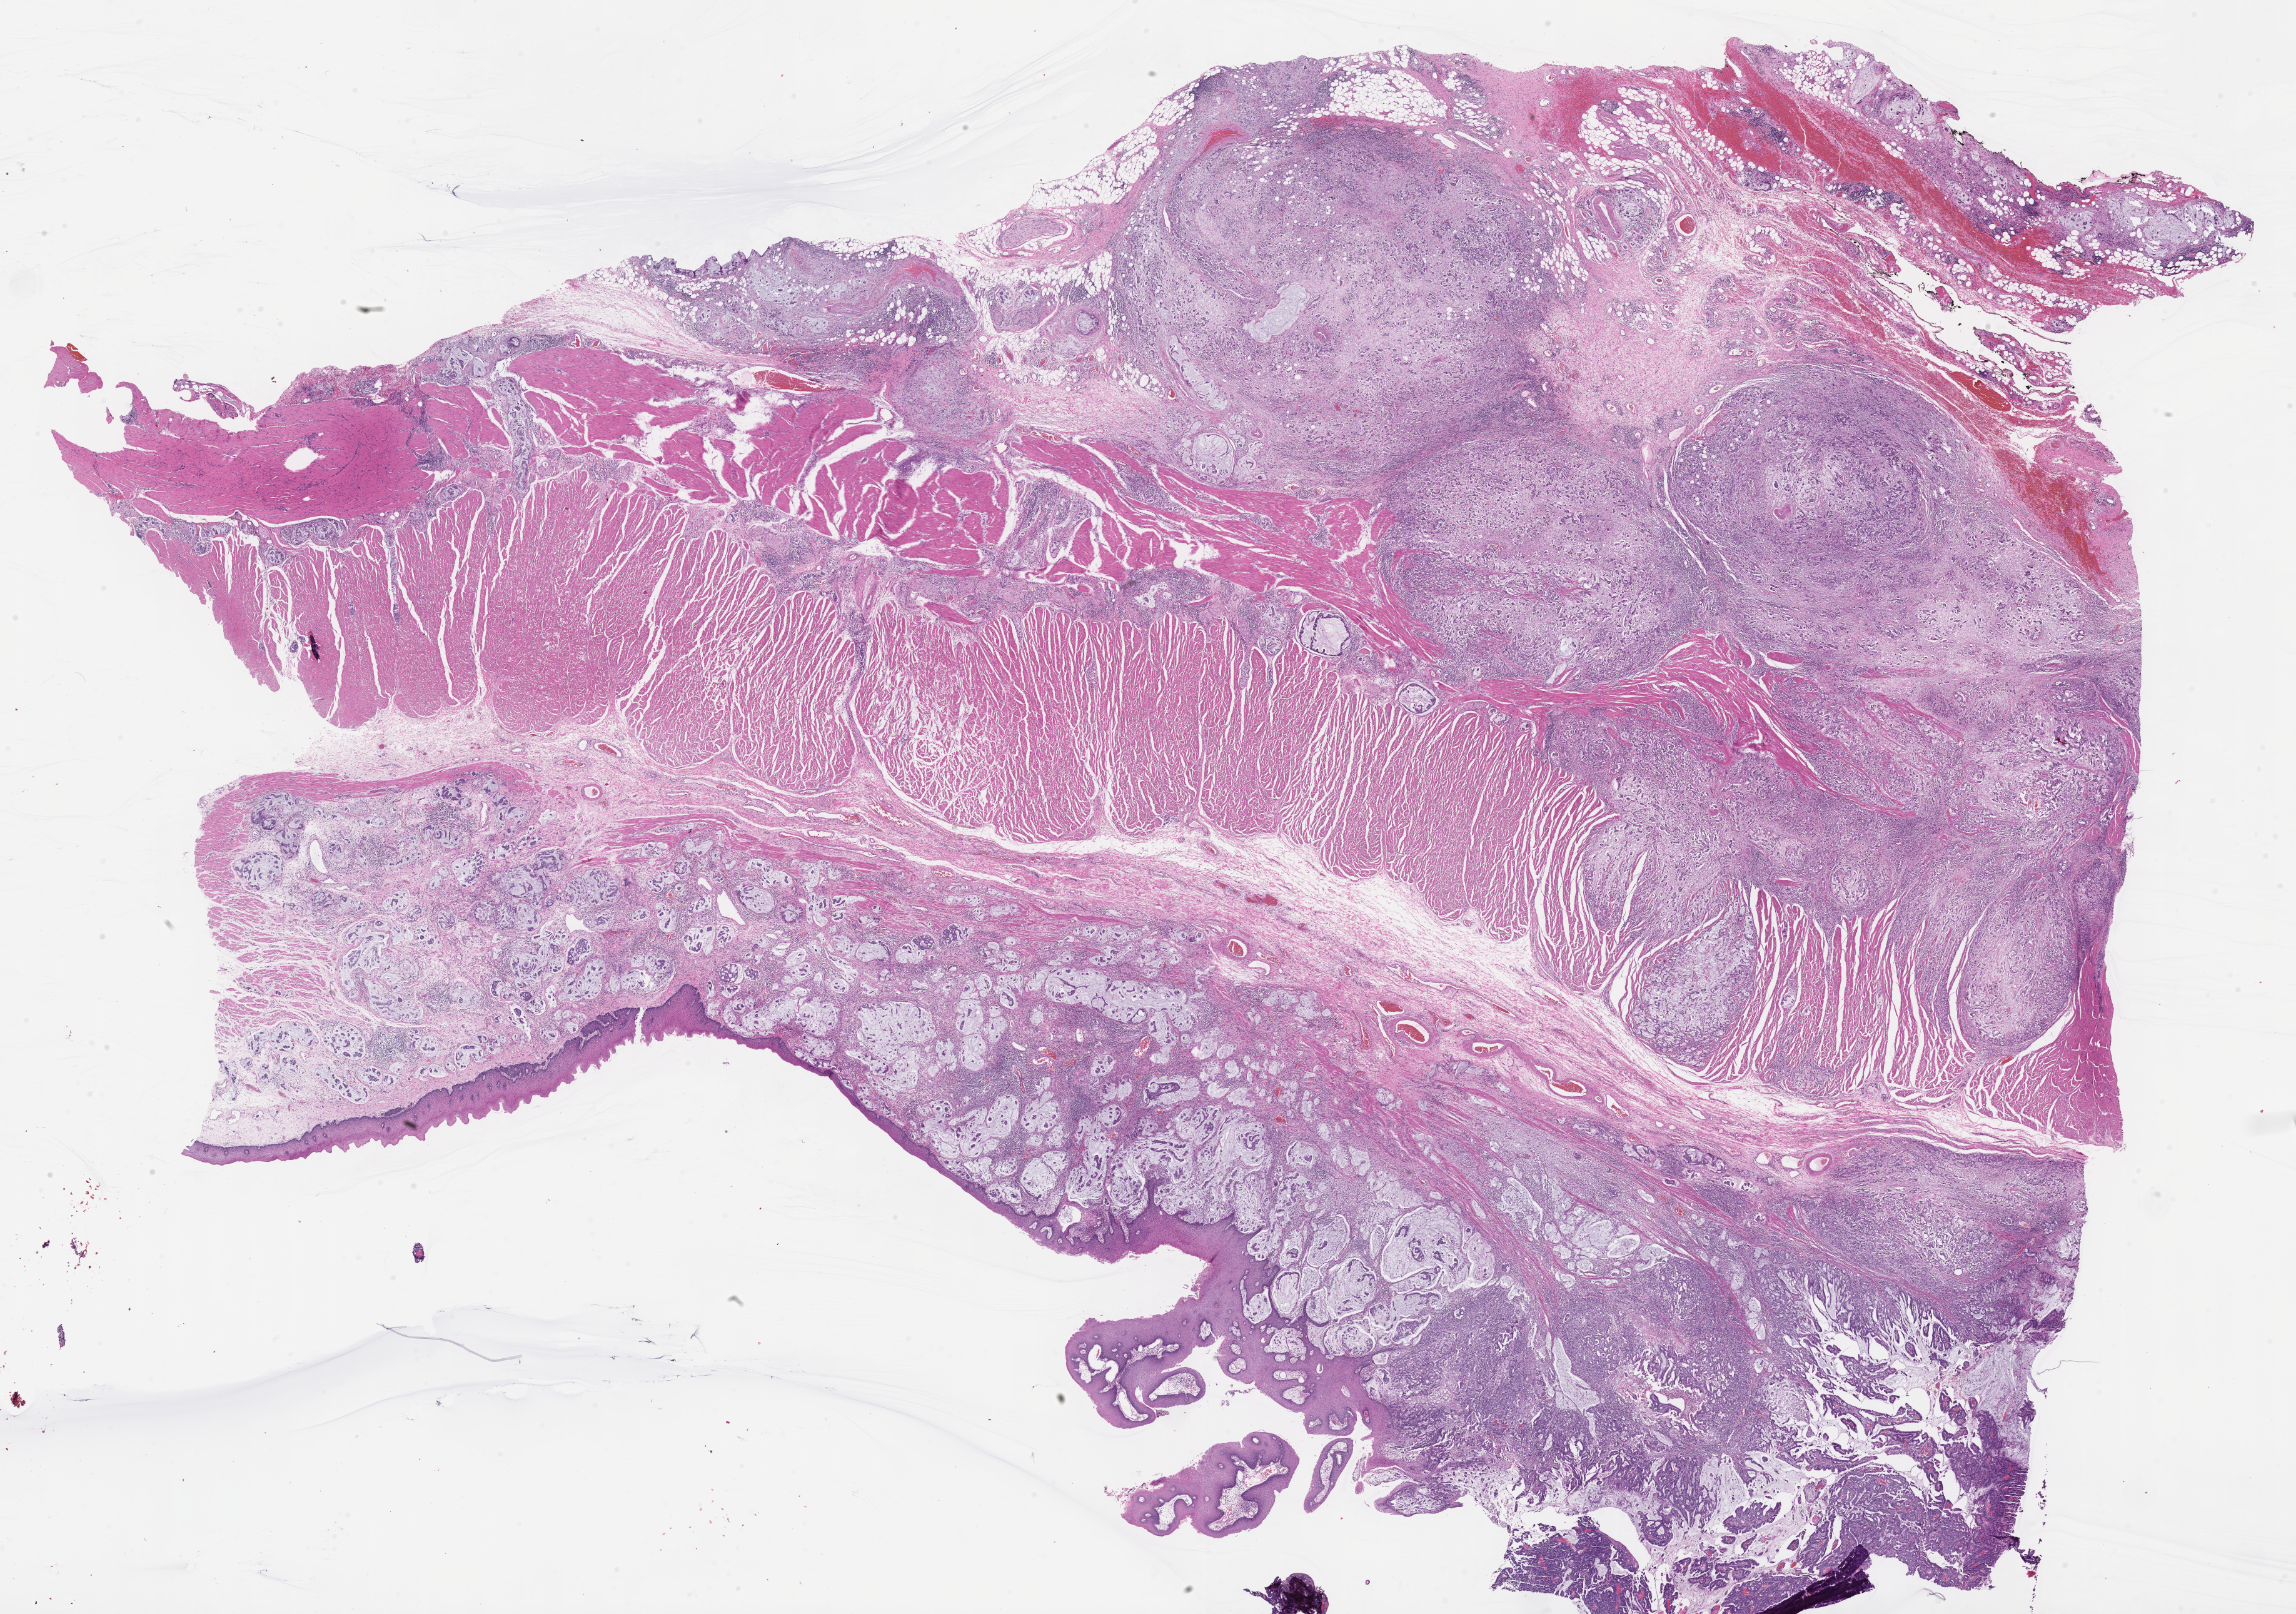
Whole-slide image, H&E stain, shown as a low-resolution overview of the whole scanned area (about 29.6 x 20.8 mm). Formalin-fixed paraffin-embedded section. Specimen: primary tumor. Male patient; age at initial diagnosis 42 years. Tumor grade: G3 (poorly differentiated). Composition of this section per pathologist review: tumor cells 75%, tumor nuclei 75%, stromal cells 21%, necrosis 2%, normal cells 2%. Infiltration values recorded for this section: lymphocyte infiltration 6%, monocyte infiltration 4%, neutrophil infiltration 5%.
• AJCC pathologic stage: Stage IIIC
• histologic diagnosis: Adenocarcinoma, NOS